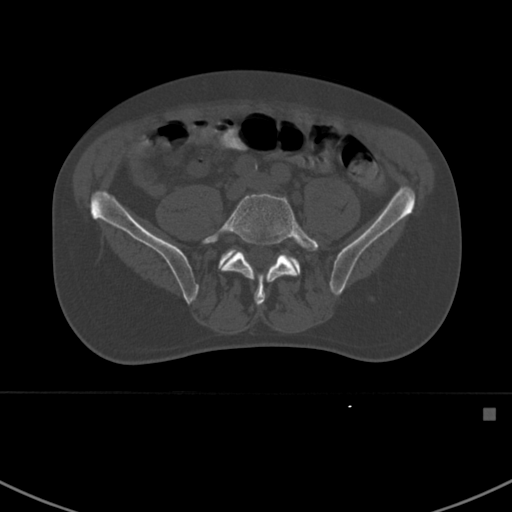
CT including the spine, one axial slice. Slice 217 of 412 in the series (ordered by position). 120 kVp. Bone window (W 1800 / L 400 HU). 1.5 mm slice thickness. 512 × 512 image matrix, field of view 358 × 358 mm. Male patient, age 59 years. Case-level facts recorded for this patient, not image findings: primary cancer: prostate.
Annotated regions visible in this slice (semi-automatic segmentation, software-assisted and operator-edited):
- L5 vertebra: bounding box [x1, y1, x2, y2] px = [202, 192, 318, 307]